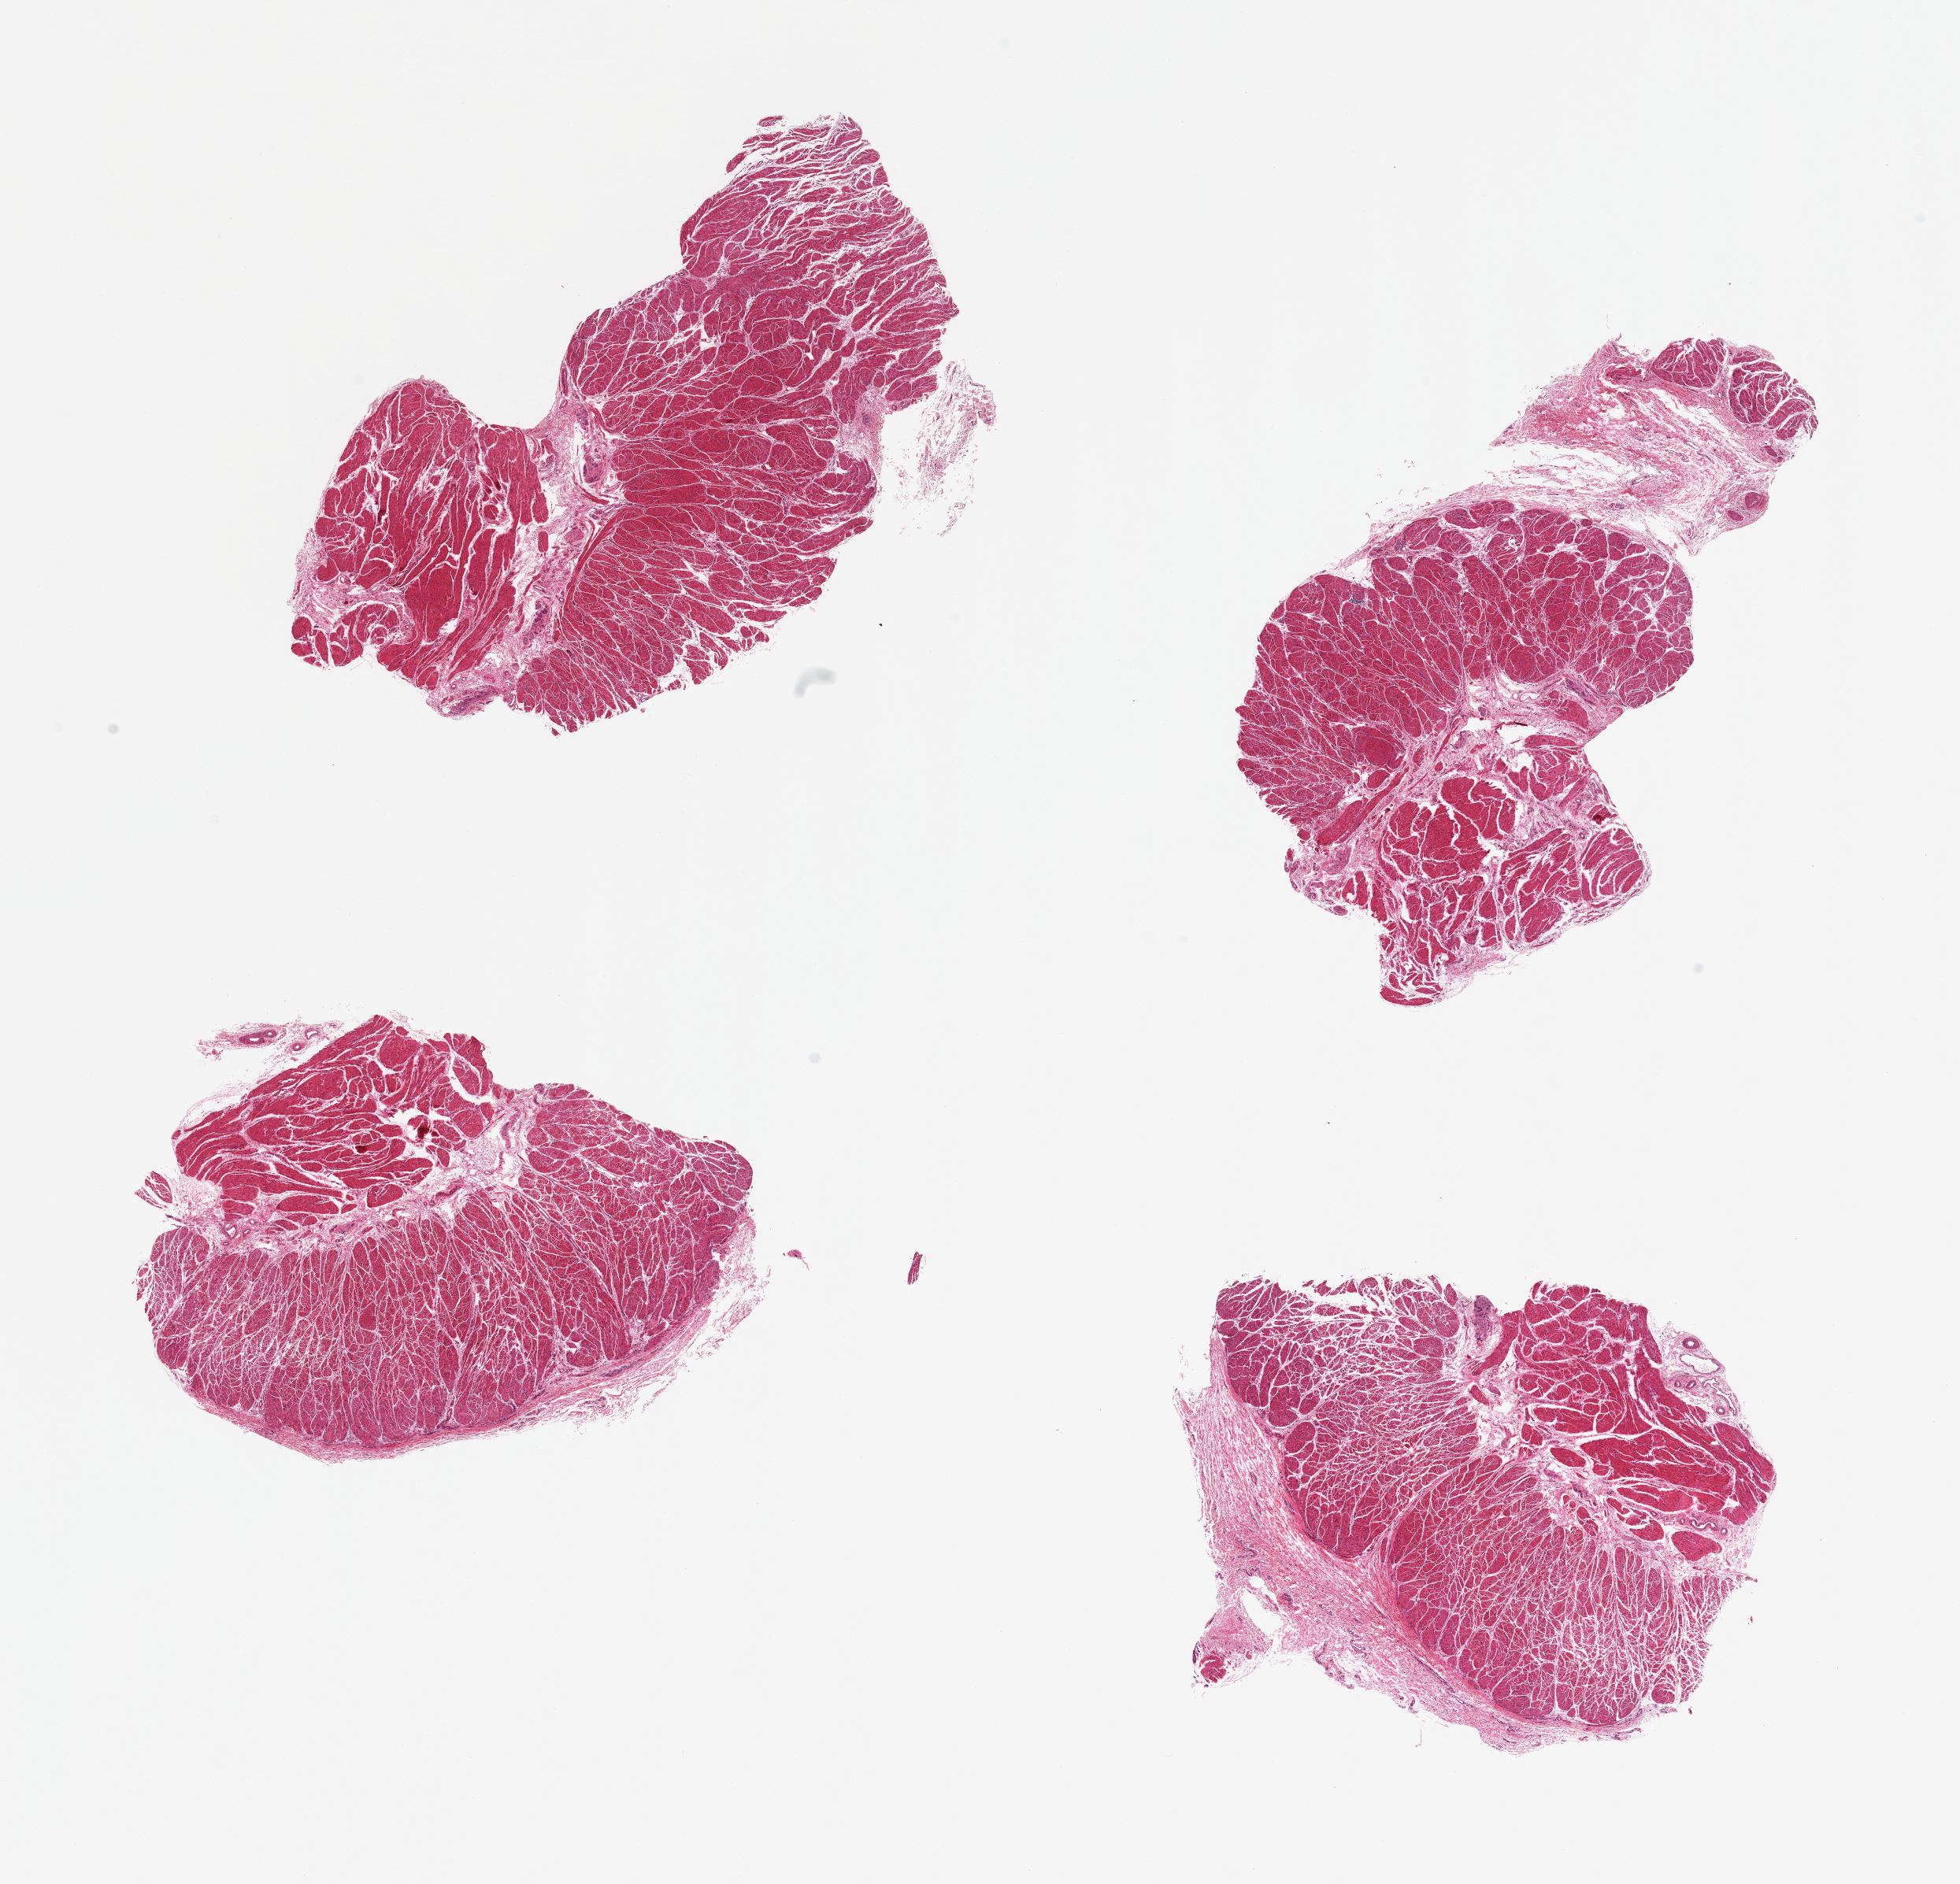
Hematoxylin and eosin (H&E) whole-slide image — low-resolution overview of the scanned area, about 19.7 x 18.9 mm, PAXgene-fixed paraffin-embedded (PFPE) section, section of gastroesophageal junction (target tissue), tissue donor sample. Donor: male.
Reviewer comment on this tissue sample: 4 pieces, muscularis, good specimens.